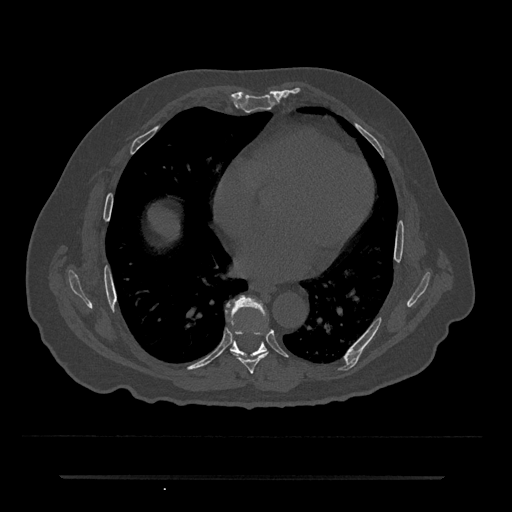
CT including the spine, one axial slice. Slice 362 of 797 in the series (ordered by position). 120 kVp. Bone window (W 1800 / L 400 HU). 0.5 mm slice thickness. 512 × 512 image matrix. Male patient, age 69 years. Case-level facts recorded for this patient, not image findings: primary cancer: prostate.
Outlined on this slice (semi-automatic segmentation, software-assisted and operator-edited):
- T7 vertebra: bounding box [x1, y1, x2, y2] px = [231, 332, 269, 374]
- T8 vertebra: [226, 296, 267, 357]